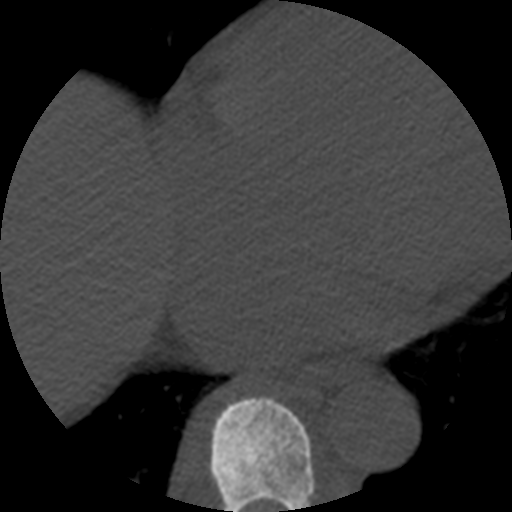
CT including the spine, one axial slice; position 312 of 508 along the scan axis; bone window (W 1800 / L 400 HU); 512 × 512 image matrix, field of view 160 × 160 mm. Patient age 57 years. Case-level facts recorded for this patient, not image findings: primary cancer: prostate.
Annotated regions visible in this slice (semi-automatic segmentation, software-assisted and operator-edited):
- T8 vertebra: bounding box [x1, y1, x2, y2] px = [209, 397, 316, 512]